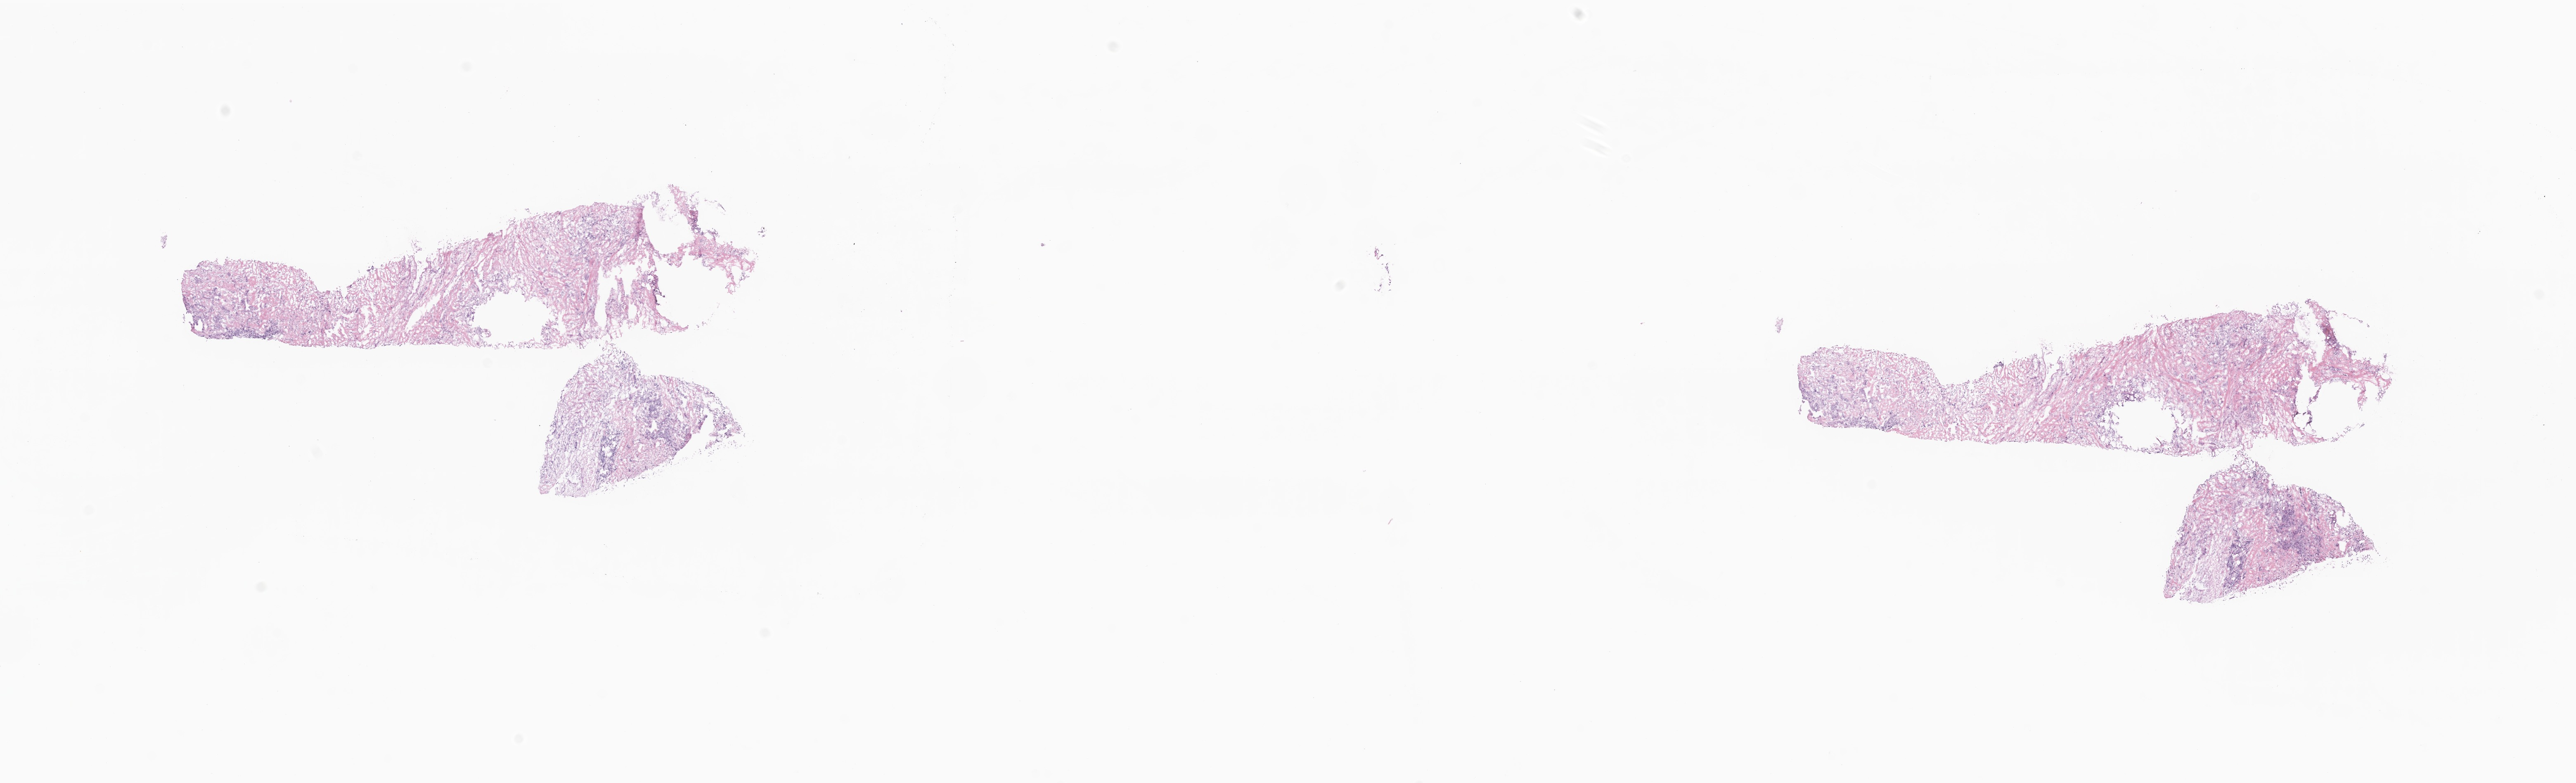
Digitized H&E-stained section — a low-resolution overview of the entire scanned area, about 26.3 x 8.0 mm, cryosection, primary tumor, anatomic site: breast (left). Female, age 66 years at initial diagnosis. Pathologist review of this section (percent, as recorded): tumor cells 100%, tumor nuclei 80%, stromal cells 0%, necrosis 0%, normal cells 0%. Inflammatory infiltration, as recorded: lymphocyte infiltration 0%, monocyte infiltration 0%, neutrophil infiltration 0%.
Histologic diagnosis: Infiltrating duct carcinoma, NOS. Section: top of the tissue portion.